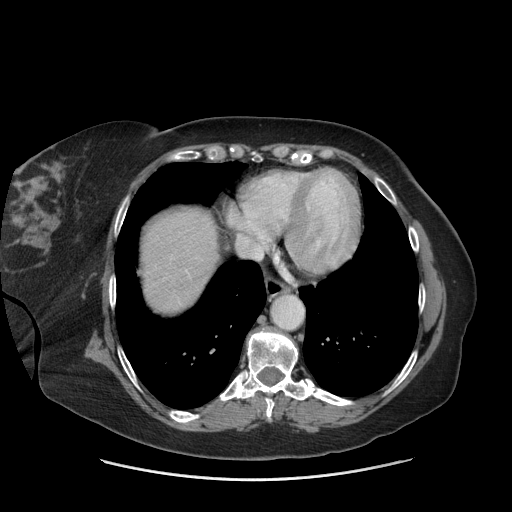
Contrast-enhanced abdominal CT (liver protocol), one axial slice; position 67 of 69 along the scan axis; 140 kVp; soft-tissue window (W 400 / L 40 HU); 2.5 mm slice thickness; 512 × 512 image matrix, field of view 420 × 420 mm. Case-level facts recorded for this patient, not image findings: diagnosis: hepatocellular carcinoma (patient treated with transarterial chemoembolisation; whether this scan precedes or follows treatment is not stated here); TNM stage (as recorded): Stage-IIIB.
Outlined on this slice (semi-automatically segmented with operator editing):
- abdominal aorta: bounding box [x1, y1, x2, y2] px = [272, 297, 302, 329]
- liver parenchyma outside the tumour (the mass and vessels are separate outlines, so this box may not span the whole liver): [142, 208, 218, 310]